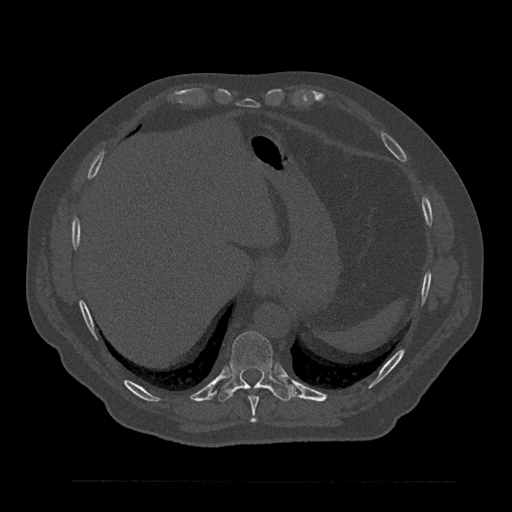
CT including the spine, one axial slice; slice 368 of 797 in the series (ordered by position); reconstruction kernel Br40s/3; bone window (W 1800 / L 400 HU); 0.5 mm slice thickness; 512 × 512 image matrix, field of view 430 × 430 mm. Male patient, age 61 years. Case-level facts recorded for this patient, not image findings: primary cancer: prostate.
Structures marked on this image (semi-automatic segmentation, software-assisted and operator-edited):
- T10 vertebra: box from (x=218, y=331) to (x=293, y=402) px
- T9 vertebra: (x=249, y=387)–(x=261, y=422)